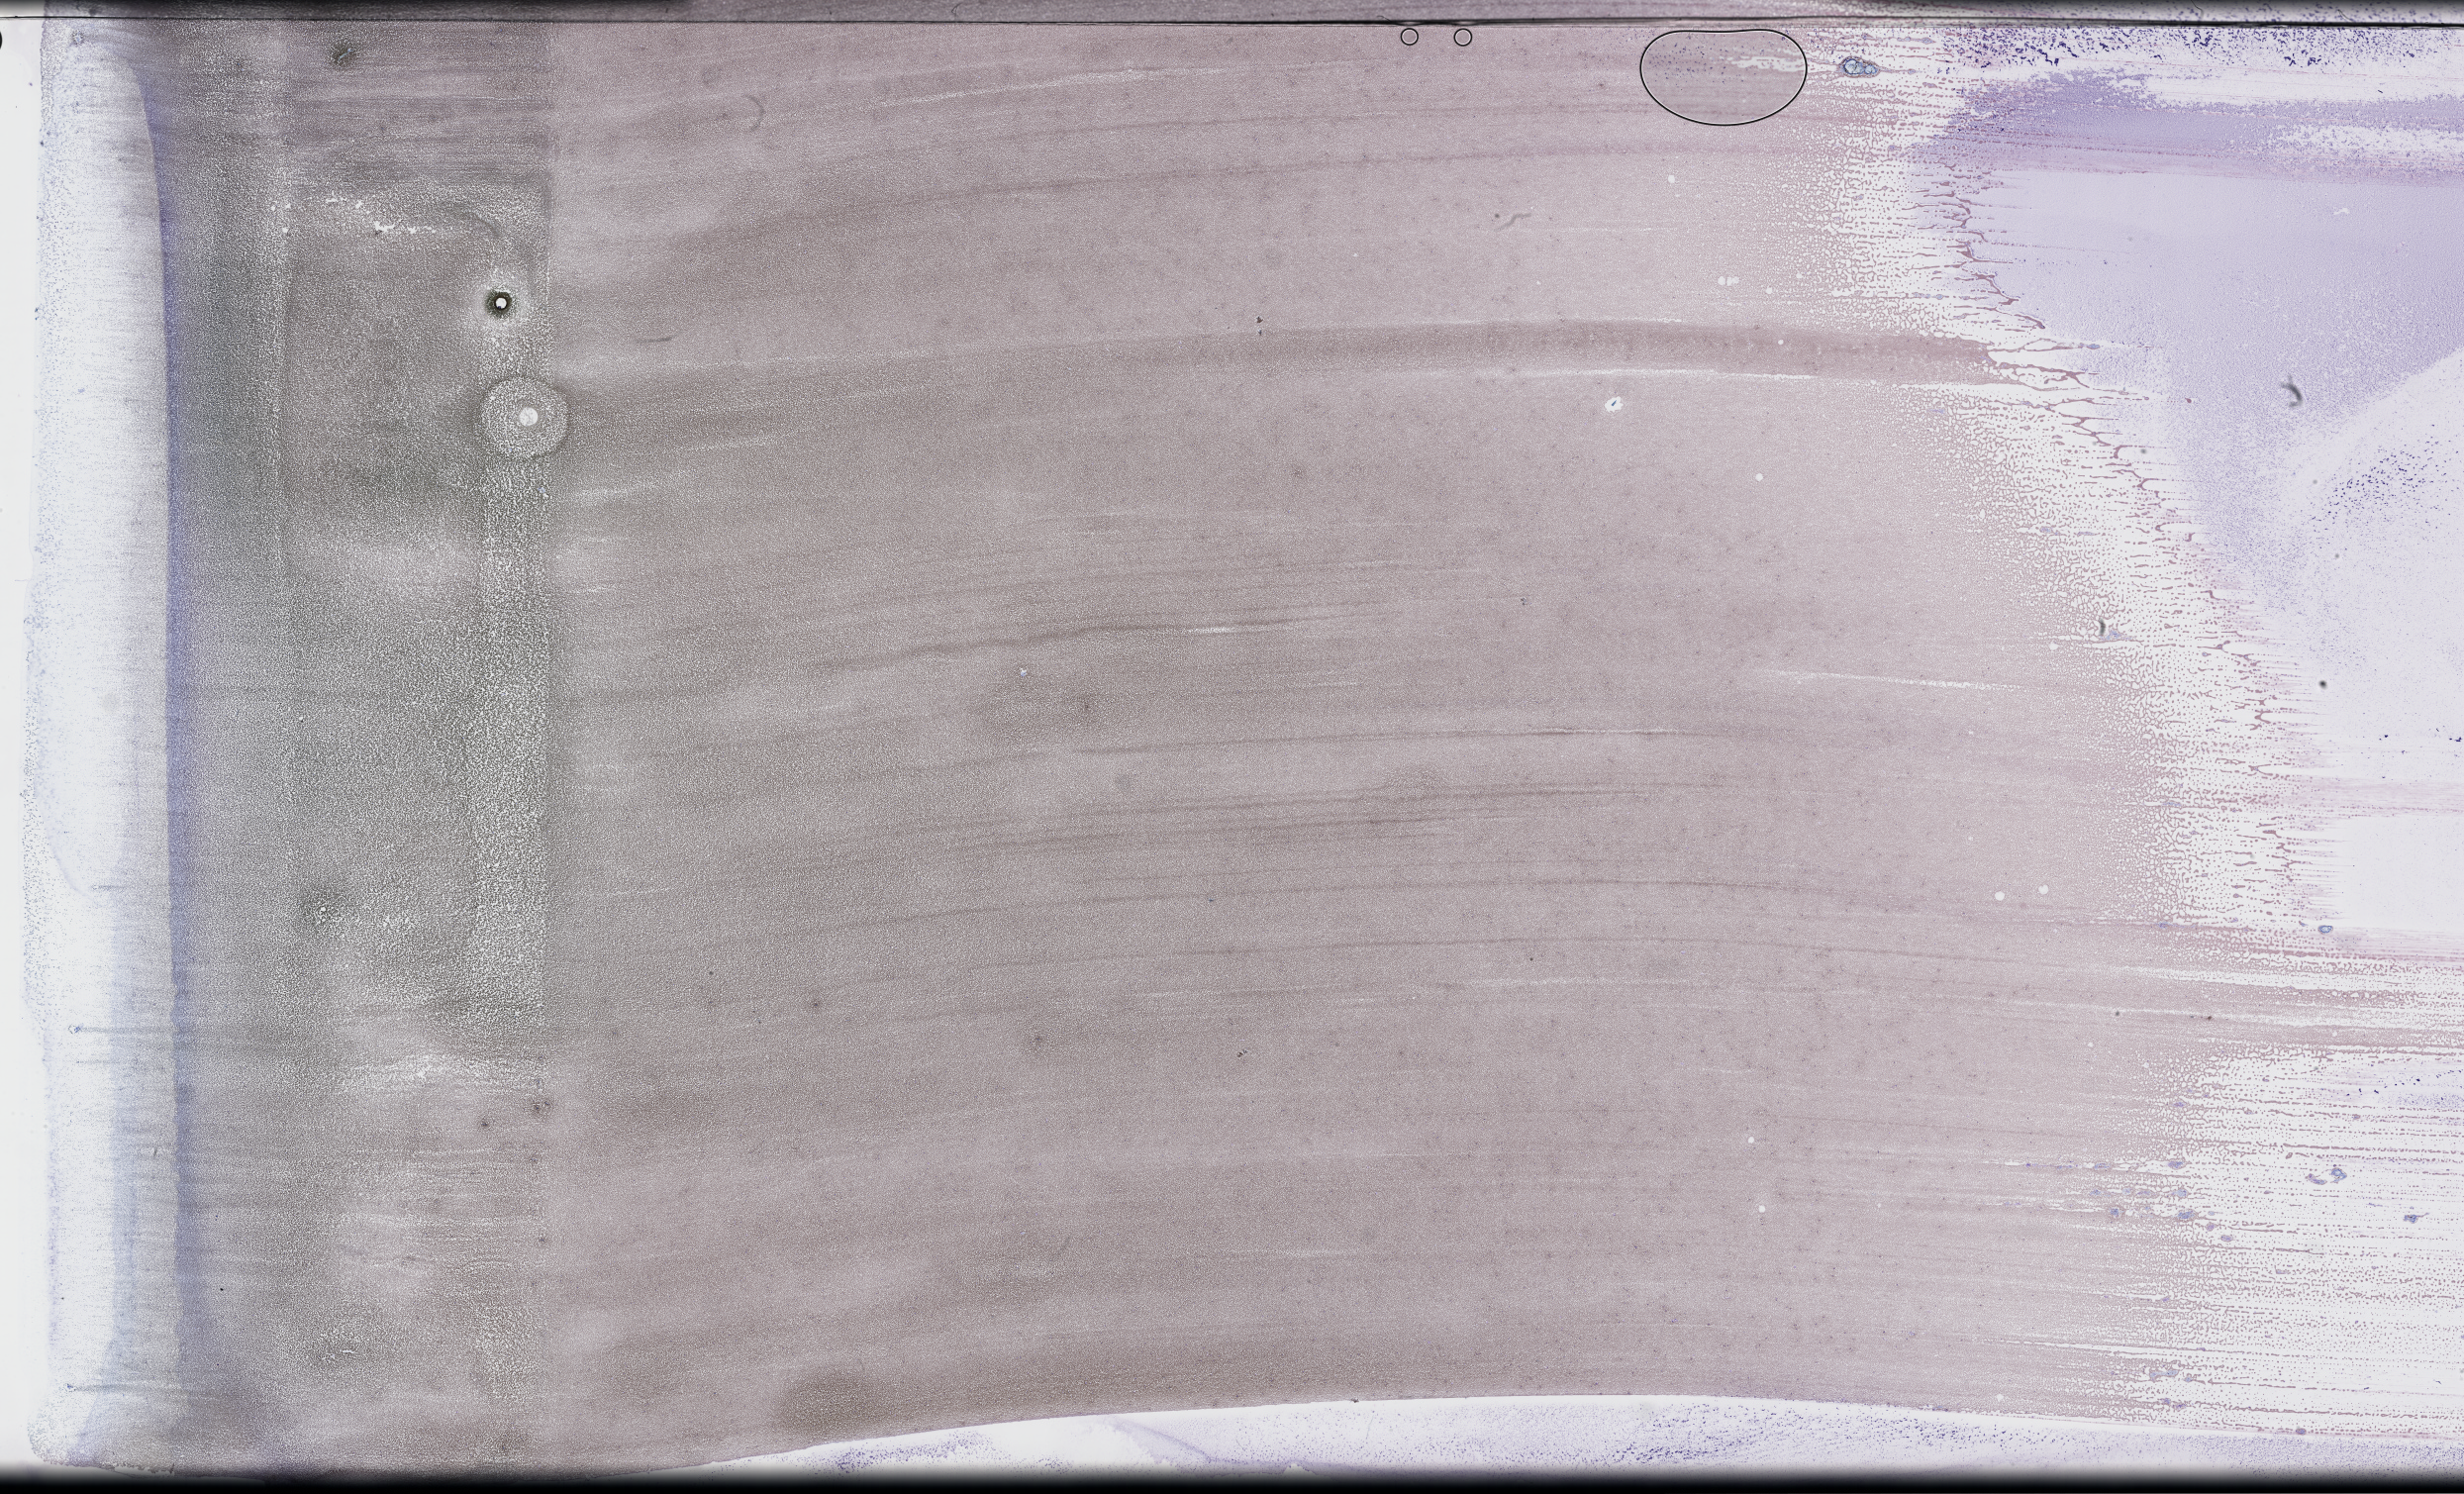
Wright–Giemsa-stained whole blood smear, whole-slide image, a low-resolution overview of the entire scanned area, about 40.2 x 24.4 mm; EDTA-anticoagulated smear; specimen time point: collected on treatment. Male patient.
- patient diagnosis: Plasma Cell Myeloma